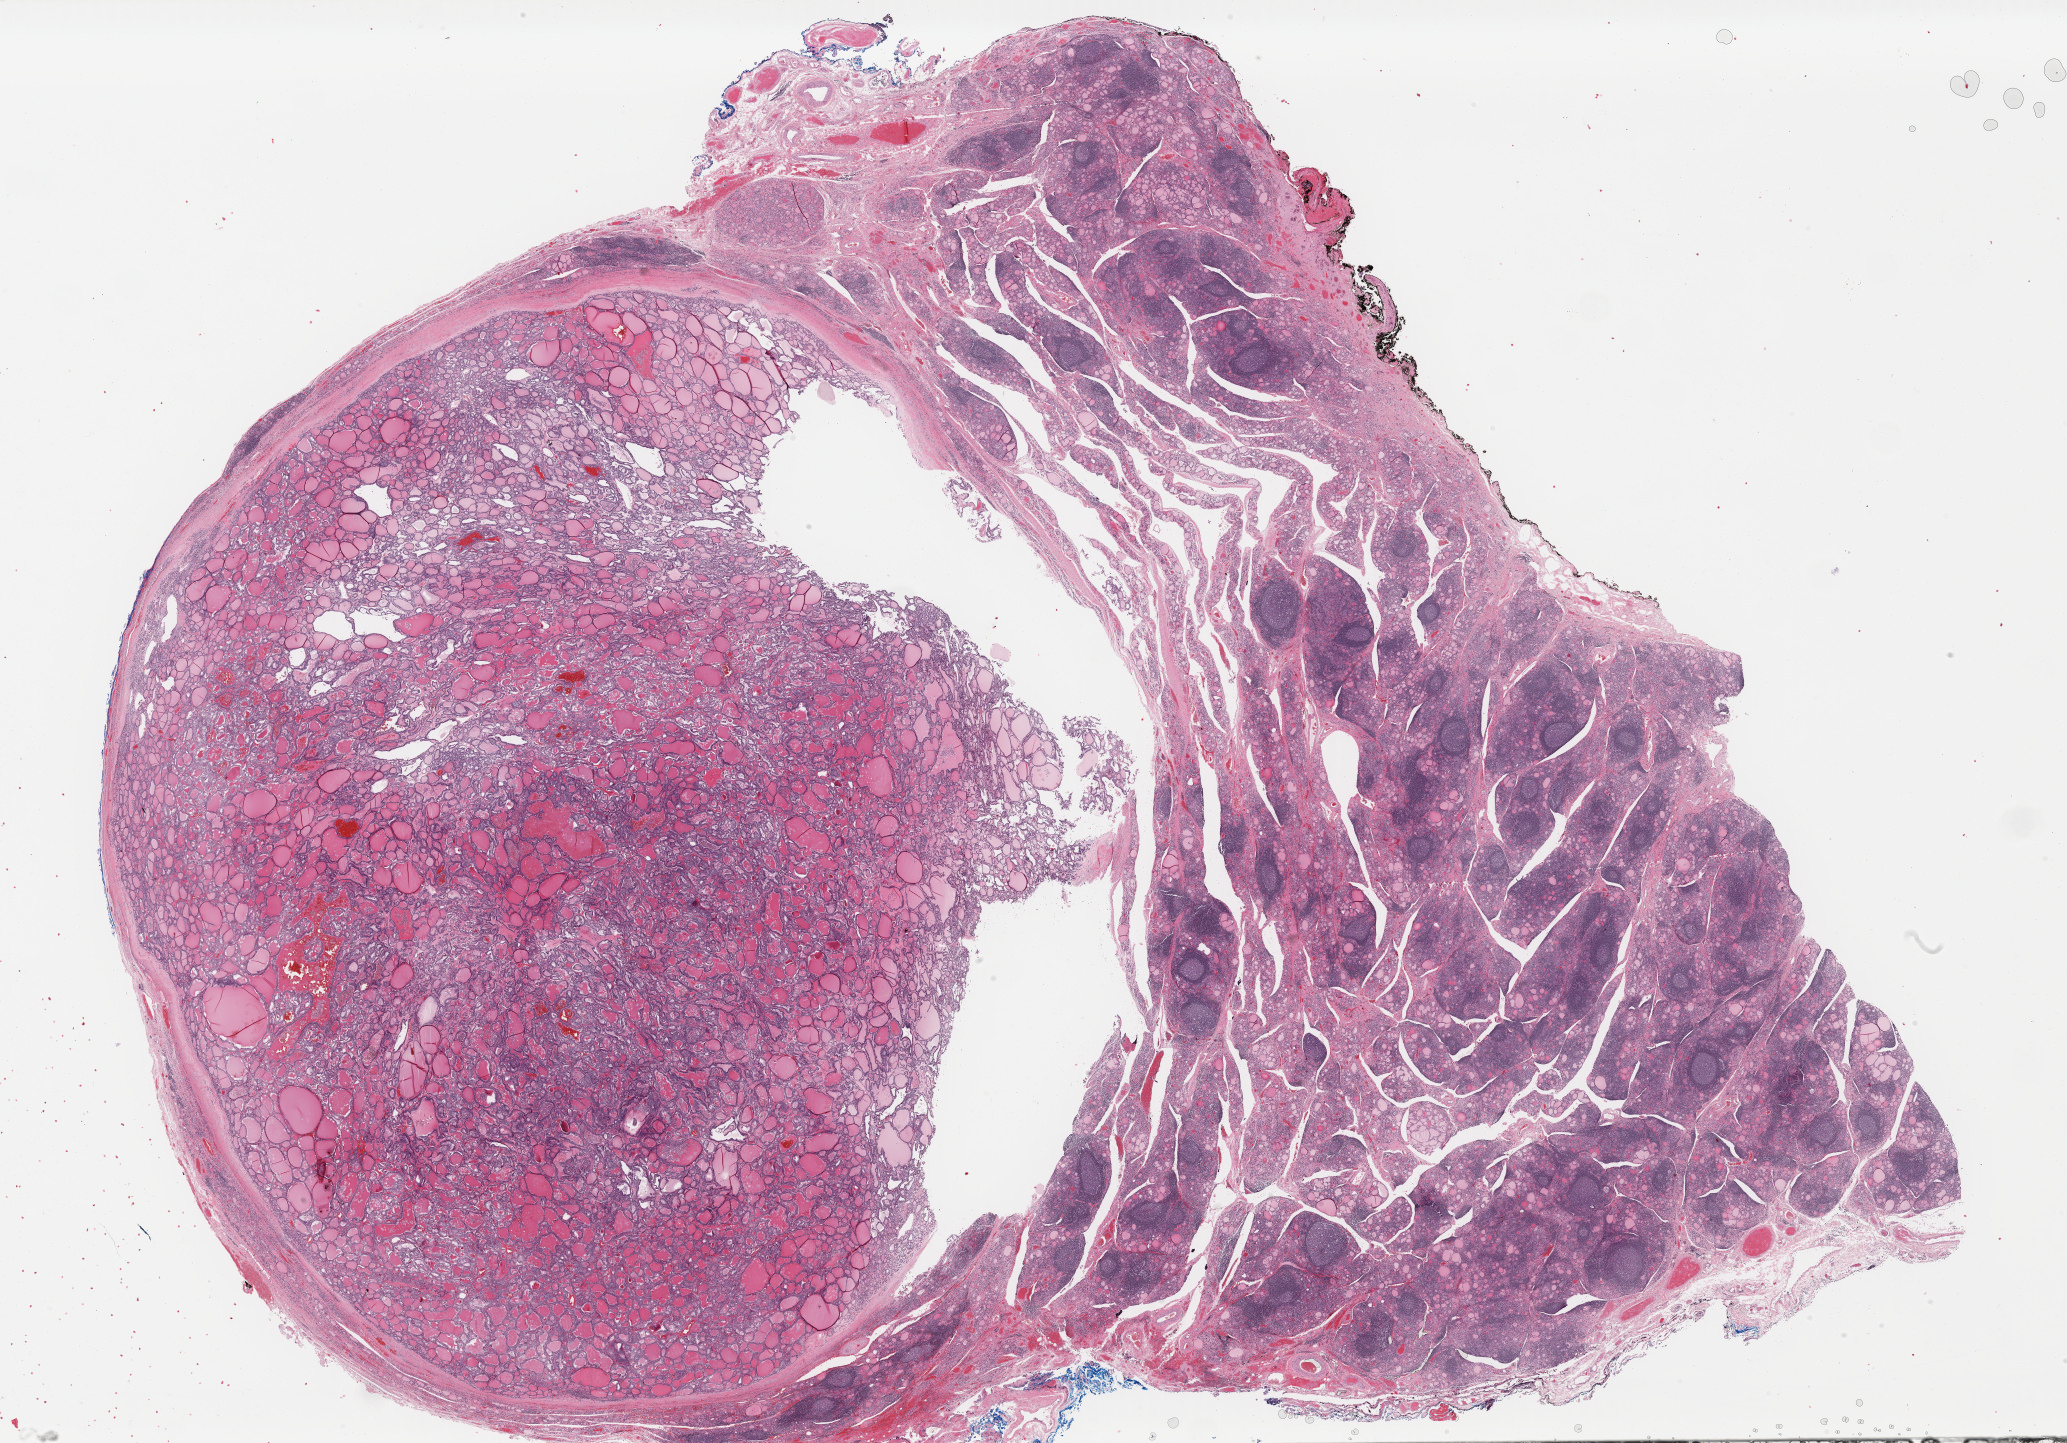
Digitized H&E tissue section (whole slide), a low-resolution overview of the entire scanned area, about 32.6 x 22.8 mm. FFPE section. Thyroid, primary tumour sample. Female patient; age at initial diagnosis 38 years.
Pathologic diagnosis: Papillary carcinoma, follicular variant (thyroid gland). TNM: T2 N0 M0. AJCC pathologic stage: I.